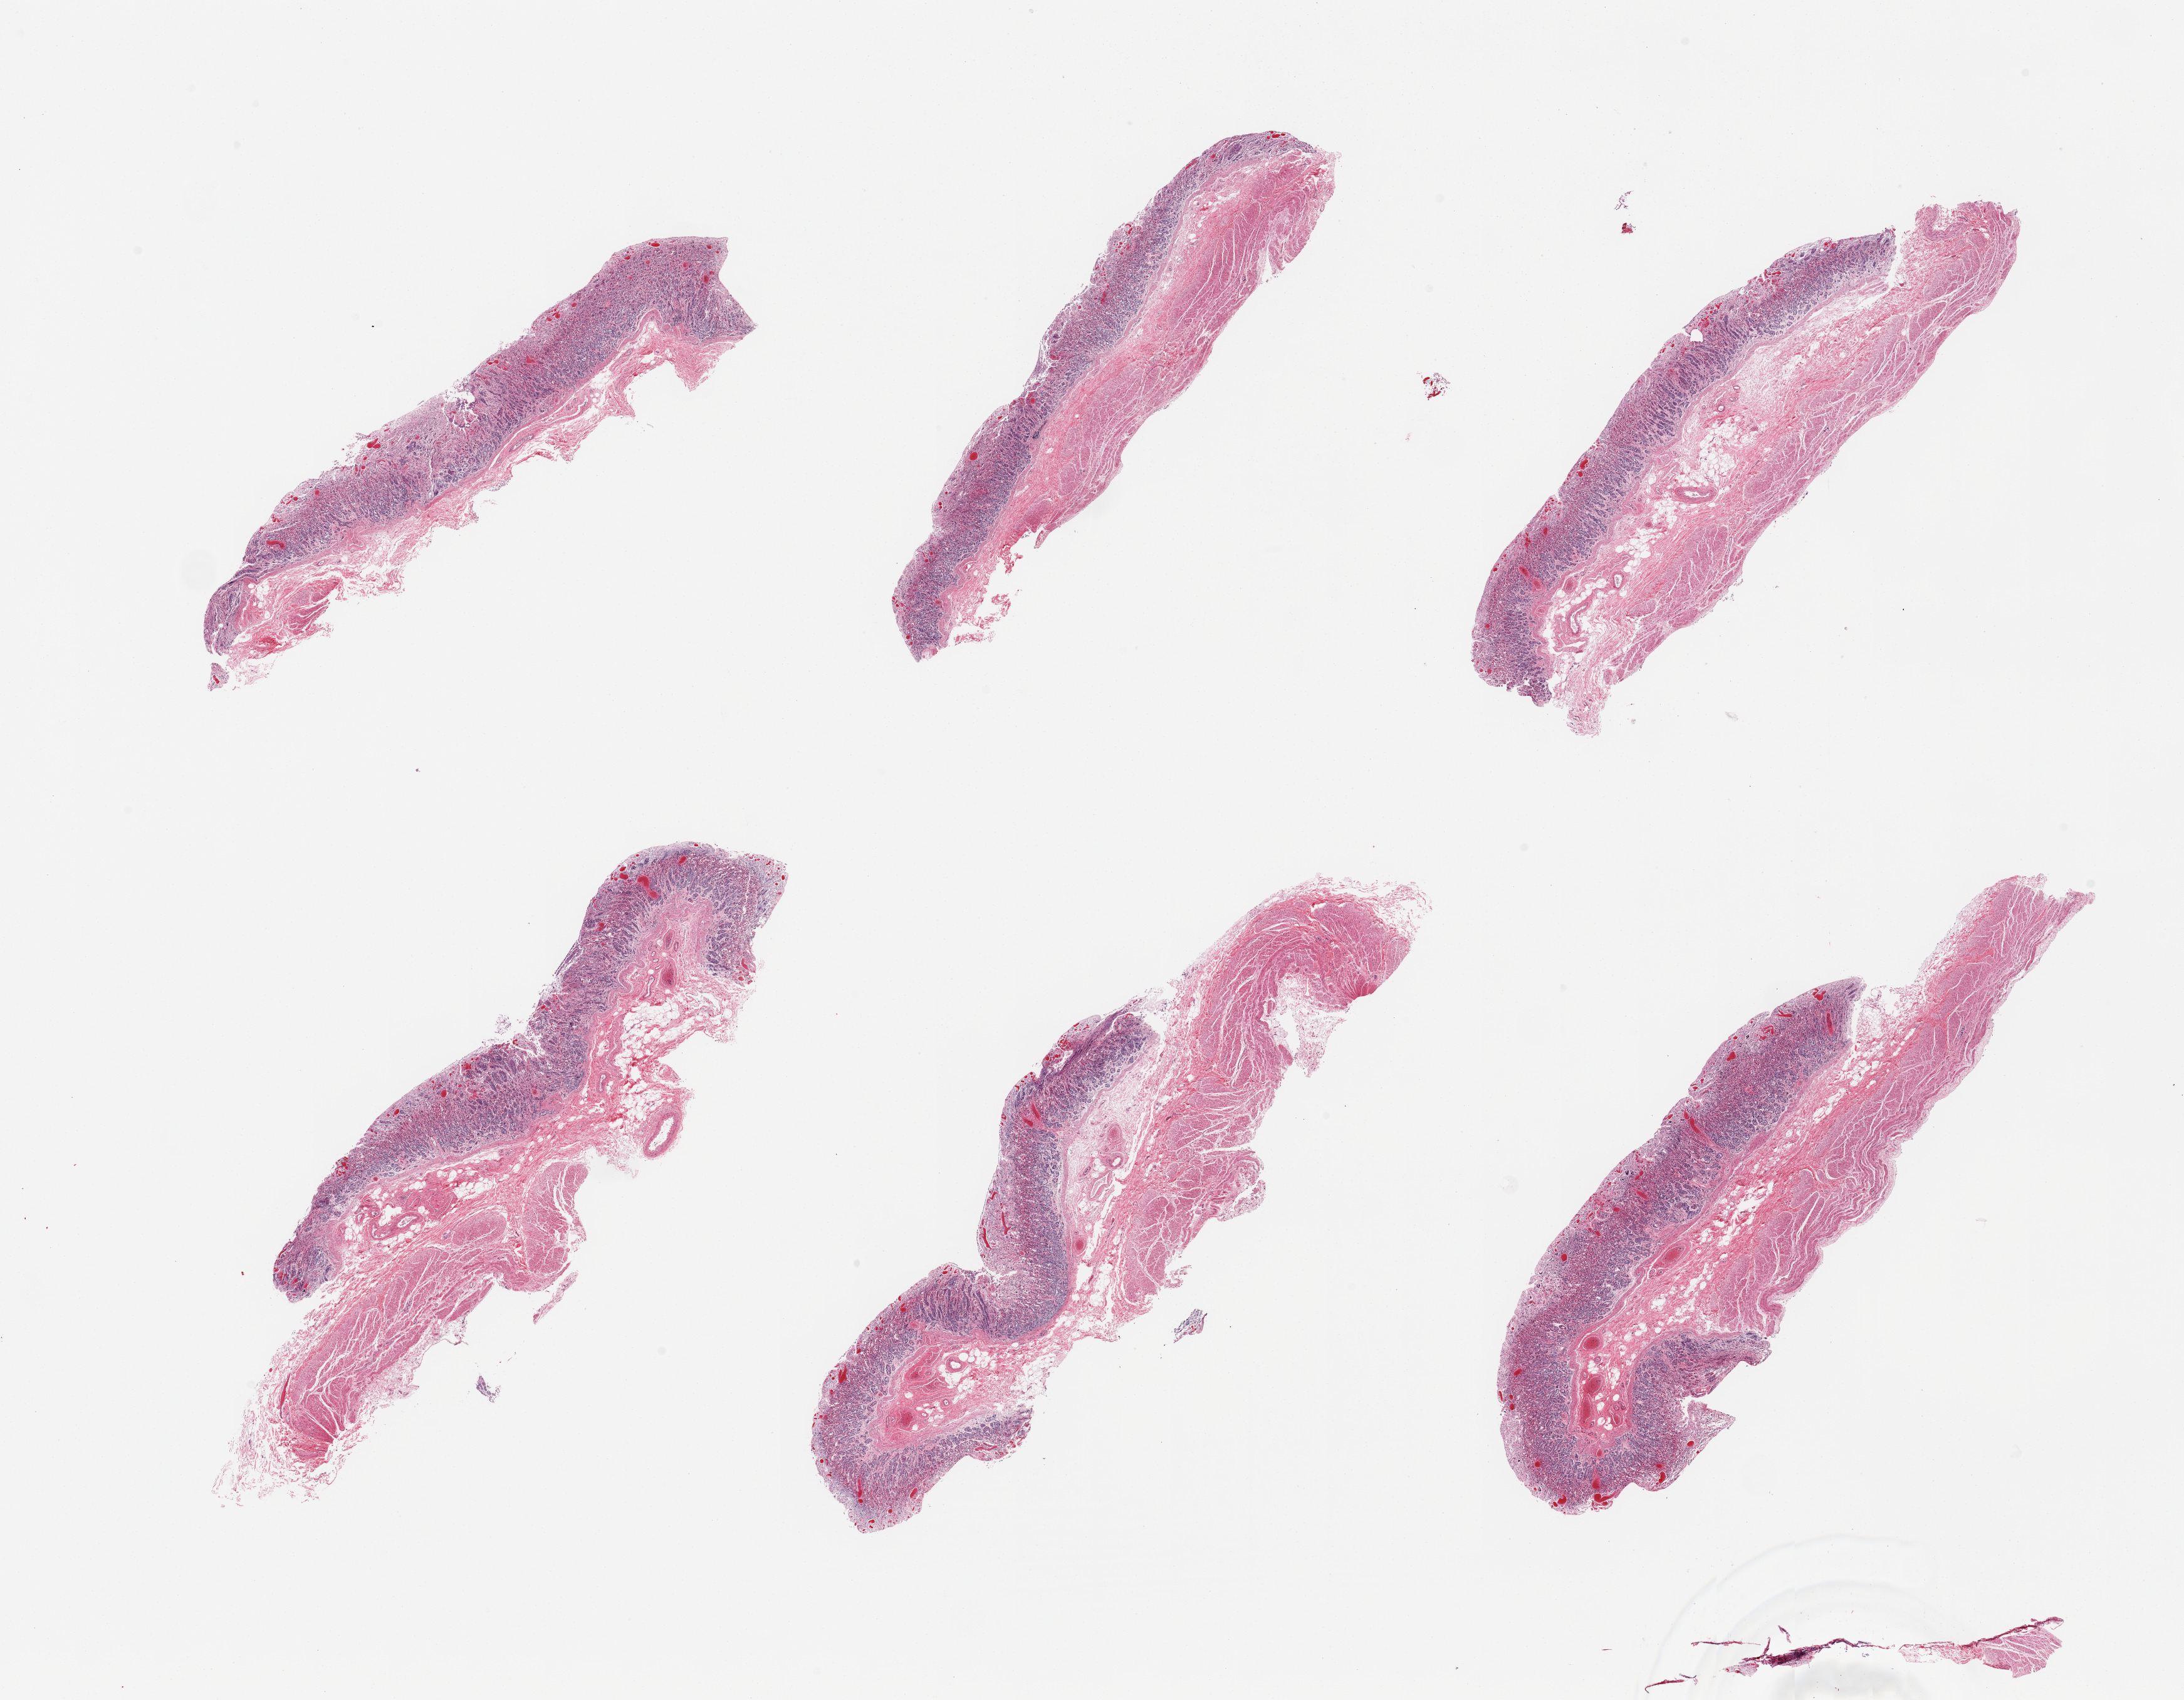
H&E whole-slide image — whole scanned area (about 27.6 x 21.5 mm, slide scanned at 20x) shown as a low-resolution overview; PAXgene-fixed paraffin-embedded (PFPE) section; section of stomach (target tissue); donor tissue sample. Donor: female.
Review note (as recorded): 6 pieces; full thickness, congestion, autloysis of superficial glands.